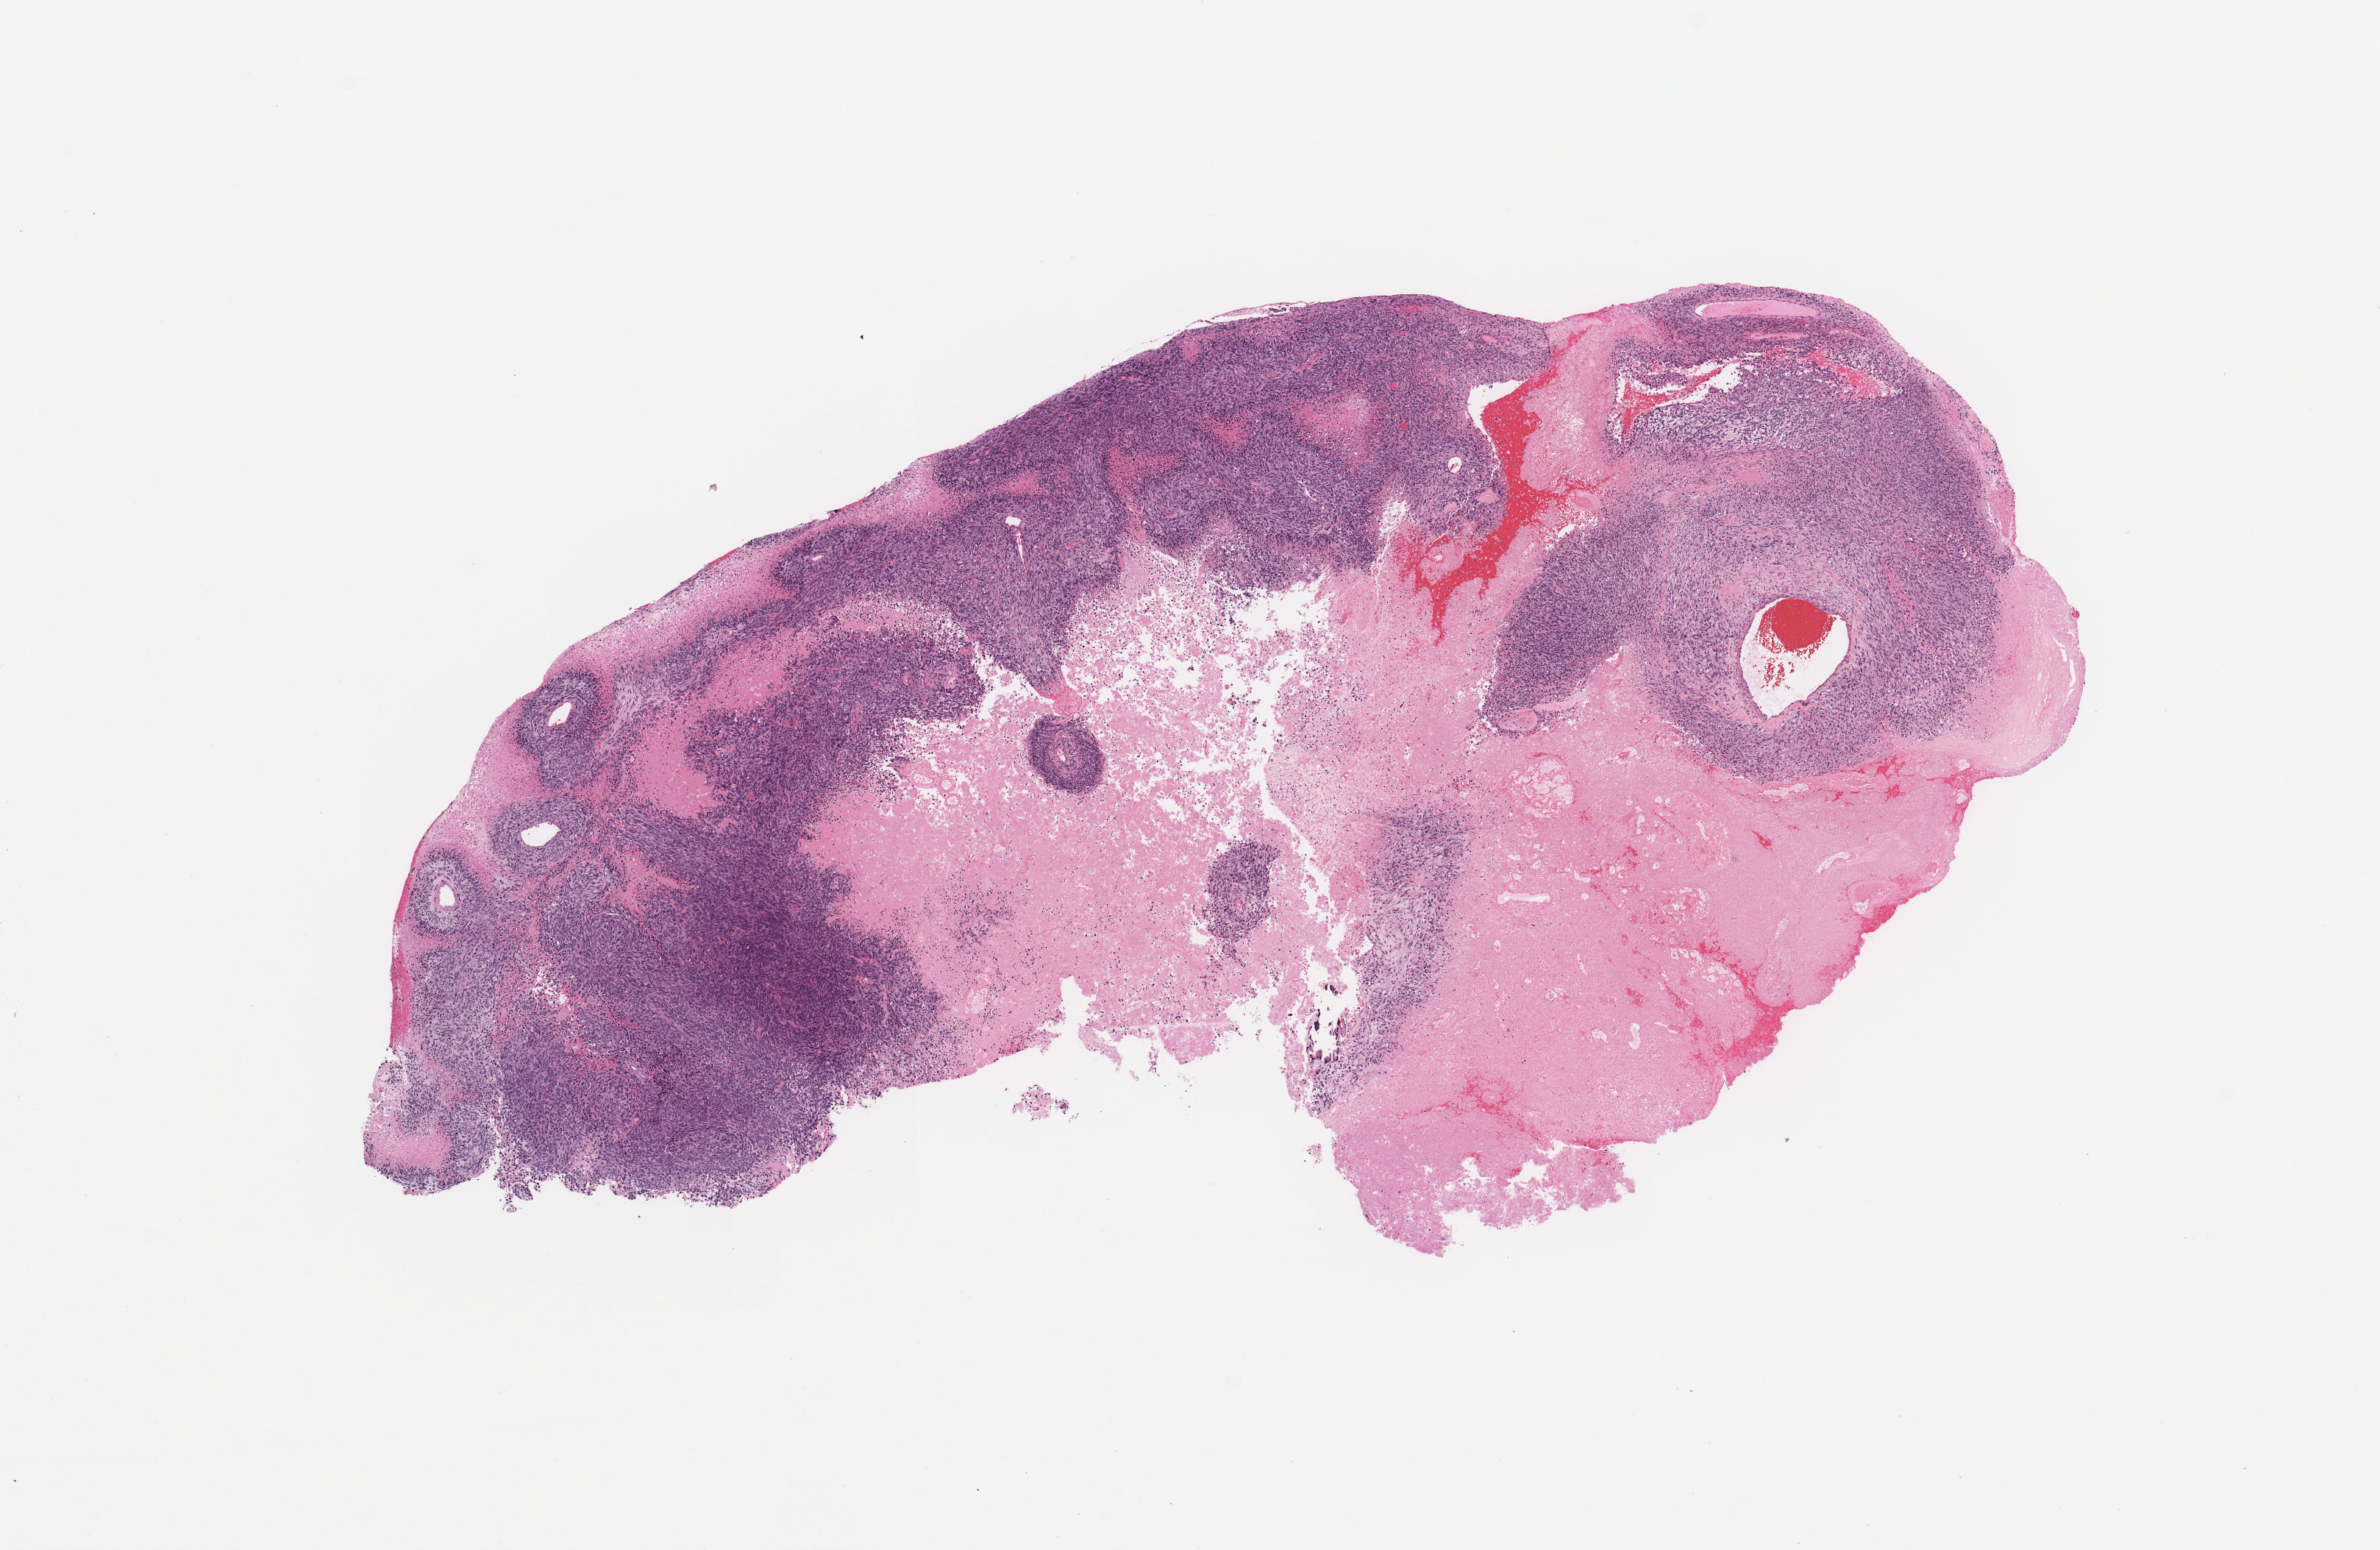
Whole-slide histology image, H&E, shown as a low-resolution overview of the whole scanned area (about 12.8 x 8.3 mm). Tumour tissue sample, brain. Female, 72 y/o.
Histologic diagnosis: Glioblastoma.